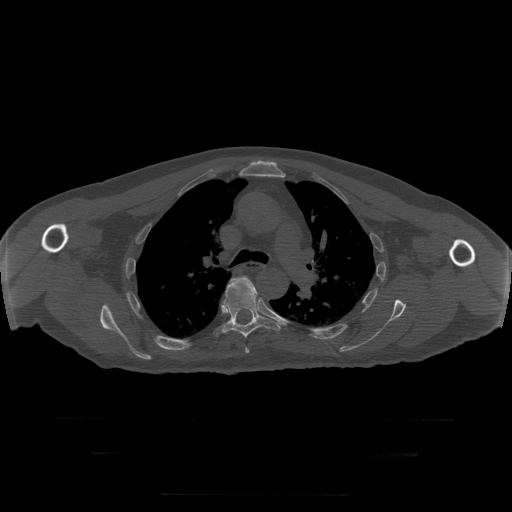
CT including the spine, one axial slice; position 211 of 397 along the scan axis; reconstruction kernel STANDARD; bone window (W 1800 / L 400 HU); 1.25 mm slice thickness; 512 × 512 image matrix, field of view 510 × 510 mm. Patient age 73 years. Case-level facts recorded for this patient, not image findings: primary cancer: prostate.
Annotated regions visible in this slice (semi-automatically segmented with operator editing):
- T5 vertebra: bounding box [x1, y1, x2, y2] px = [245, 348, 250, 354]
- T6 vertebra: [215, 276, 281, 339]